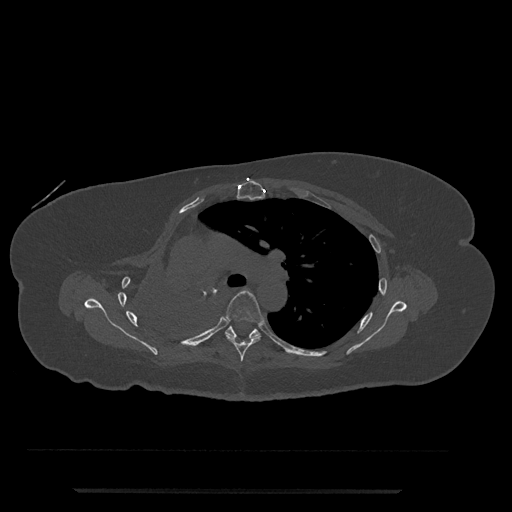
CT including the spine, one axial slice. Slice 525 of 797 in the series (ordered by position). Reconstruction kernel Br40s/3. 120 kVp. Bone window (W 1800 / L 400 HU). 0.5 mm slice thickness. 512 × 512 image matrix, field of view 440 × 440 mm. Female patient, age 51 years. Case-level facts recorded for this patient, not image findings: primary cancer: neuro.
Outlined on this slice (semi-automatic segmentation, software-assisted and operator-edited):
- T5 vertebra: bounding box [x1, y1, x2, y2] px = [224, 290, 274, 362]
- T6 vertebra: [225, 326, 260, 339]